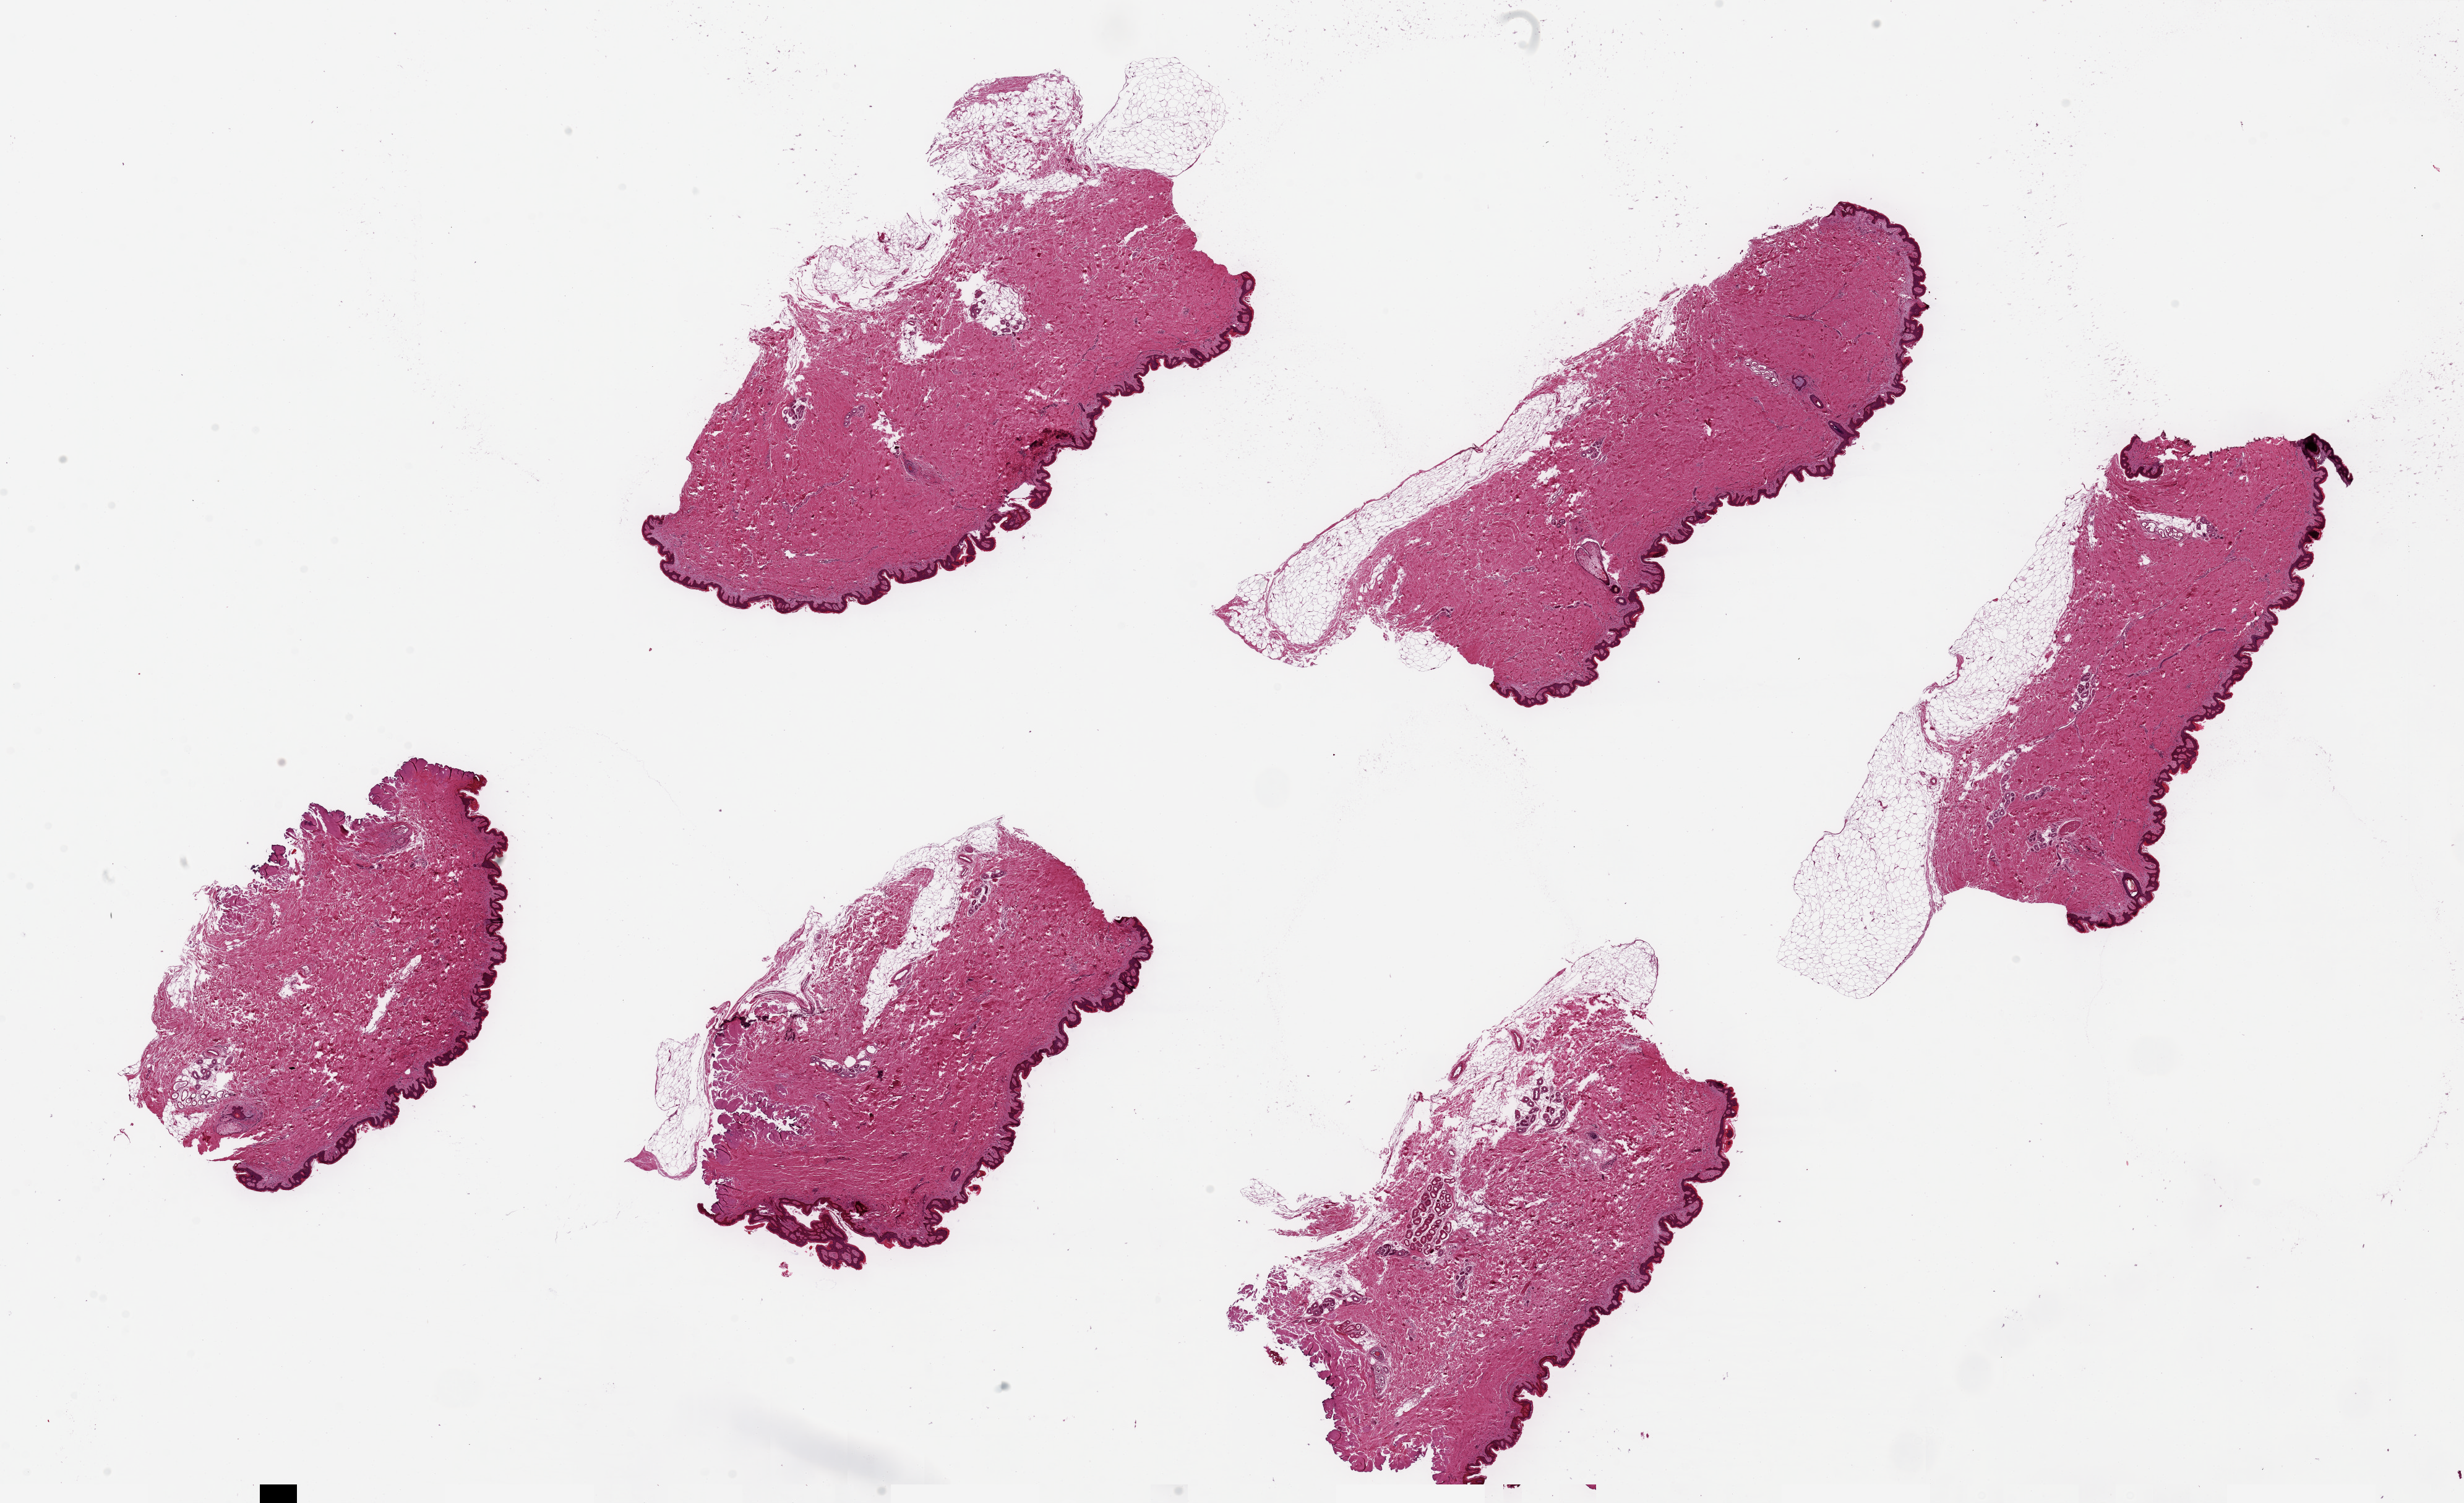
Whole-slide image, H&E stain — shown as a low-resolution overview of the whole scanned area (about 31.5 x 19.2 mm). PAXgene-fixed paraffin-embedded (PFPE) section. Section of skin of suprapubic region (target tissue). Tissue donor sample. Male donor.
* review note (as recorded): 6 pieces, up to 10x4mm; too much subcutaneous adipose (up to 1 mm)